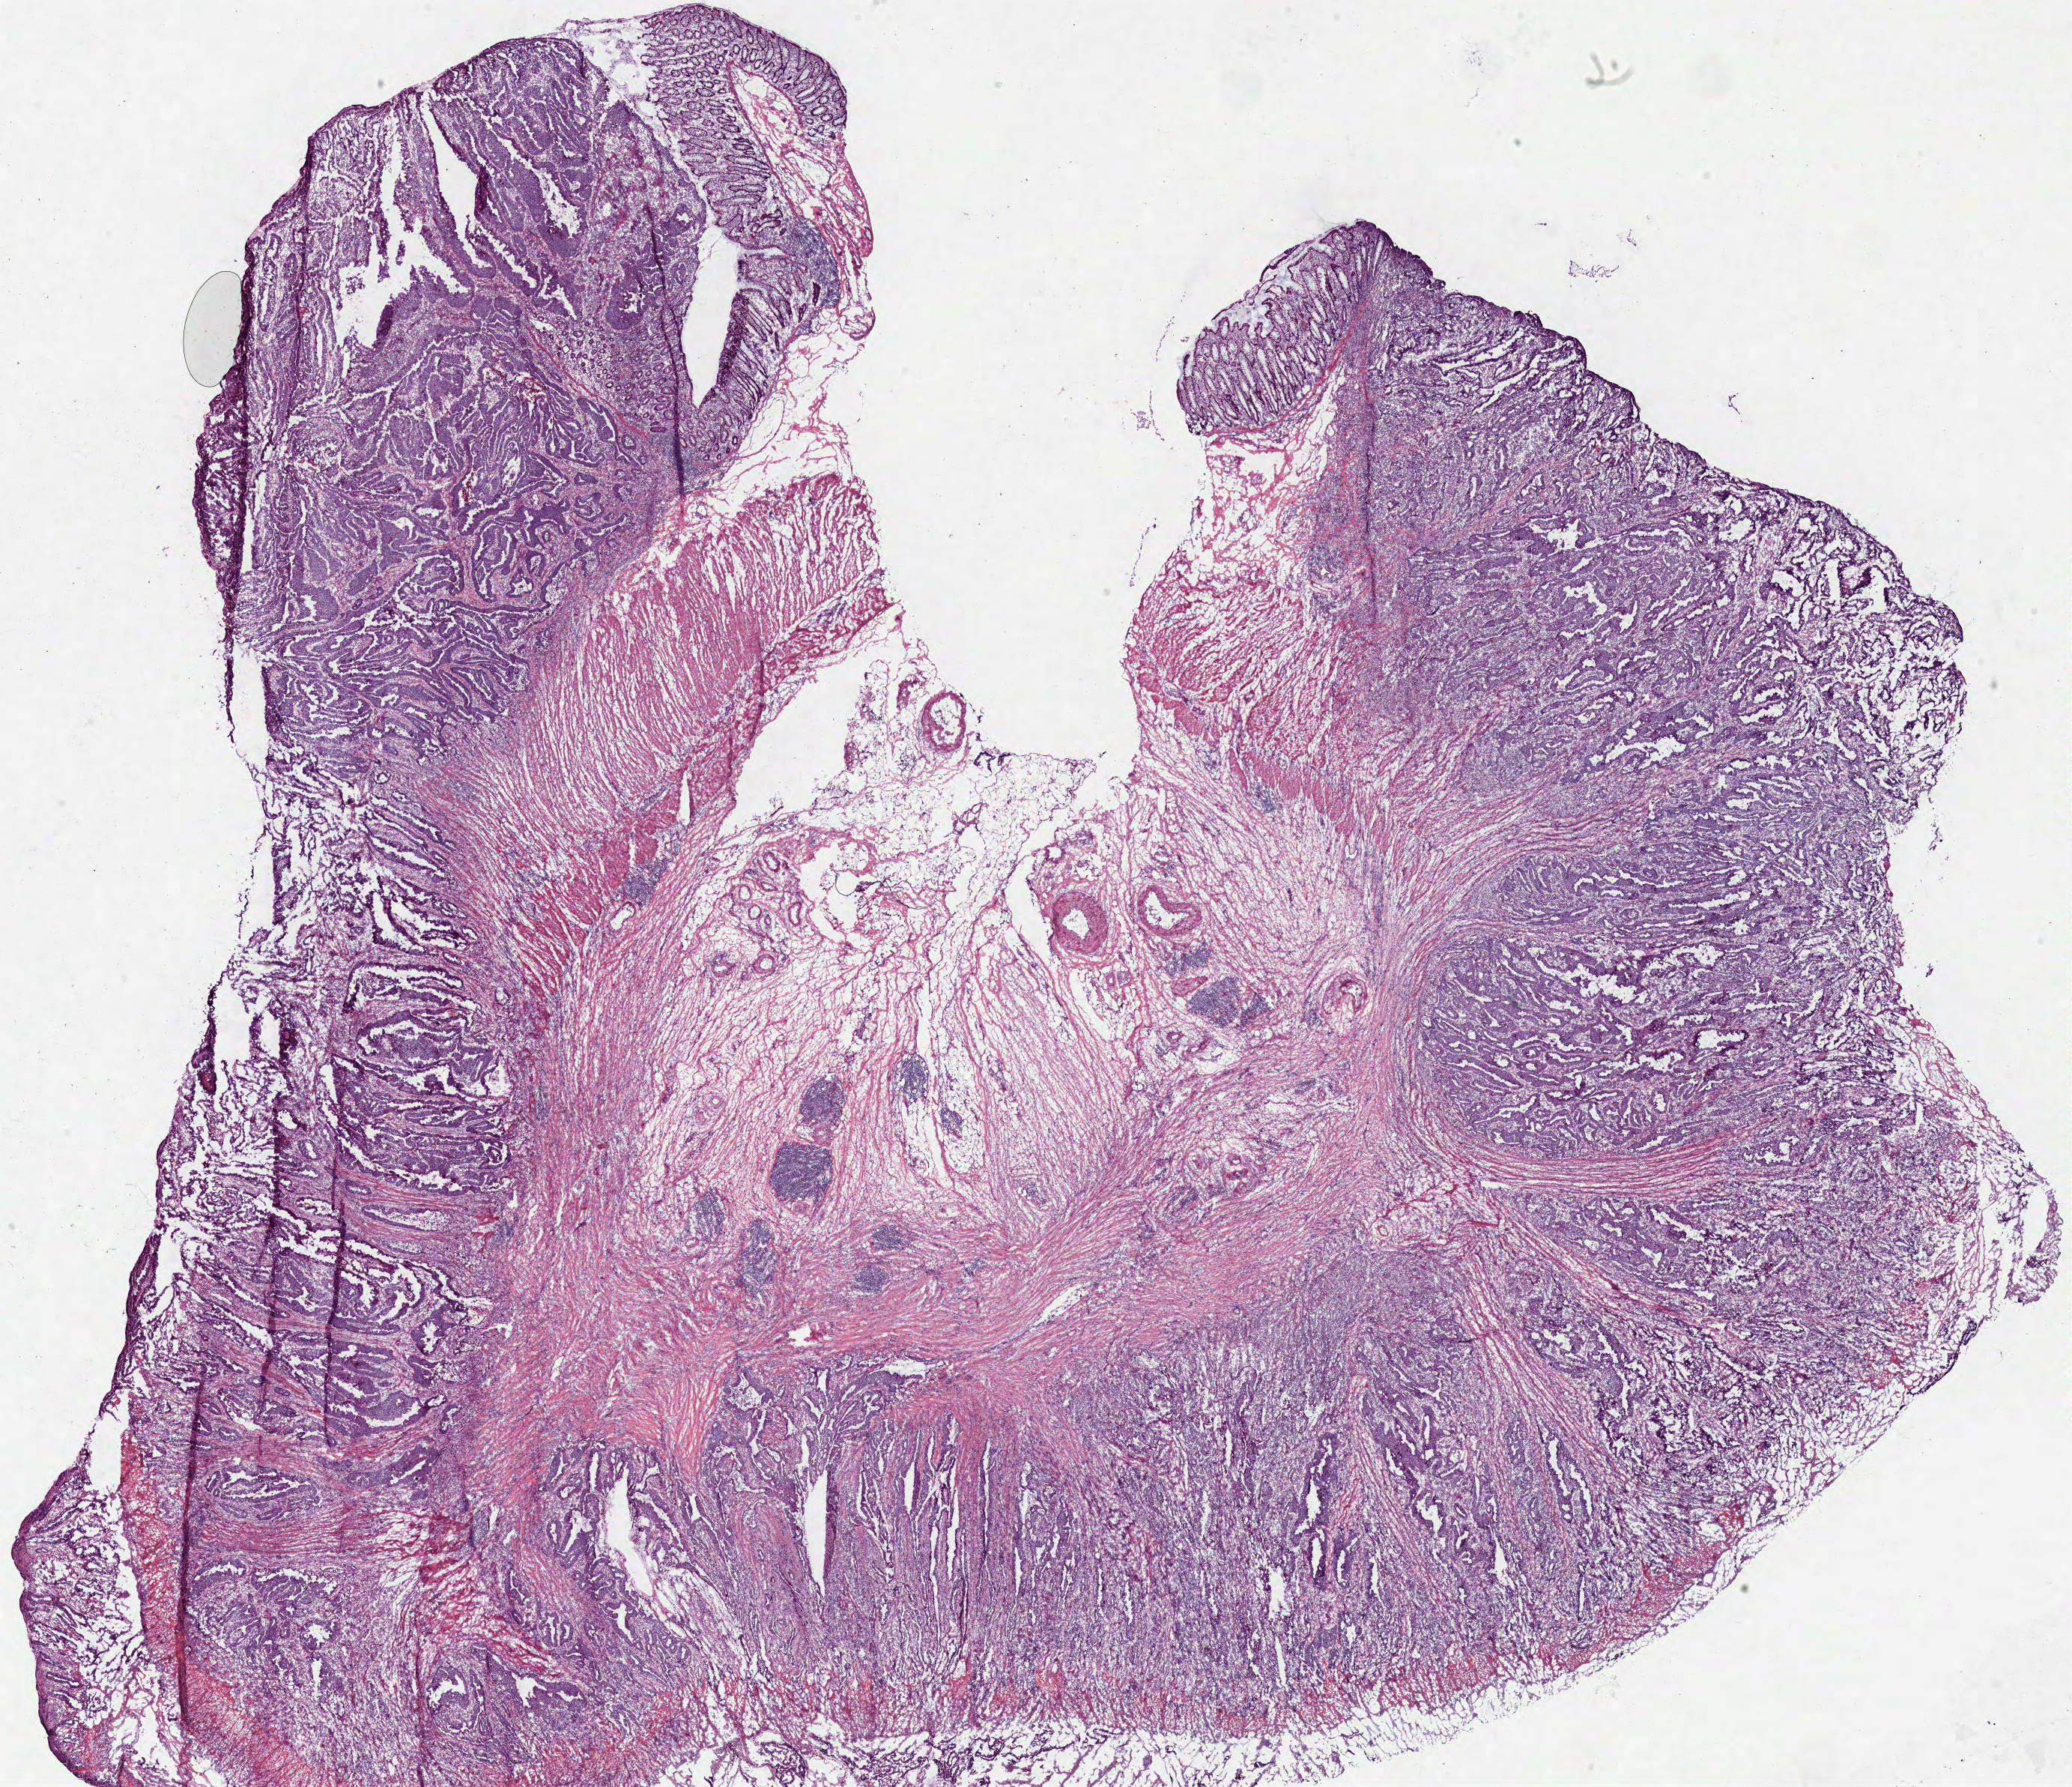
Digitized H&E tissue section (whole slide), whole scanned area (about 21.8 x 18.8 mm, slide scanned at 40x) shown as a low-resolution overview; frozen section; sample: primary tumour, colon. Female patient; age at initial diagnosis 51 years. Slide review estimates, as recorded: tumour cells 62%, tumour nuclei 80%, normal cells 5%, stromal cells 30%, necrosis 3%.
AJCC pathologic stage: IIIC (7th edition). Histologic diagnosis: Adenocarcinoma, NOS. Lymph nodes positive (case pathology): 12 of 12 examined.